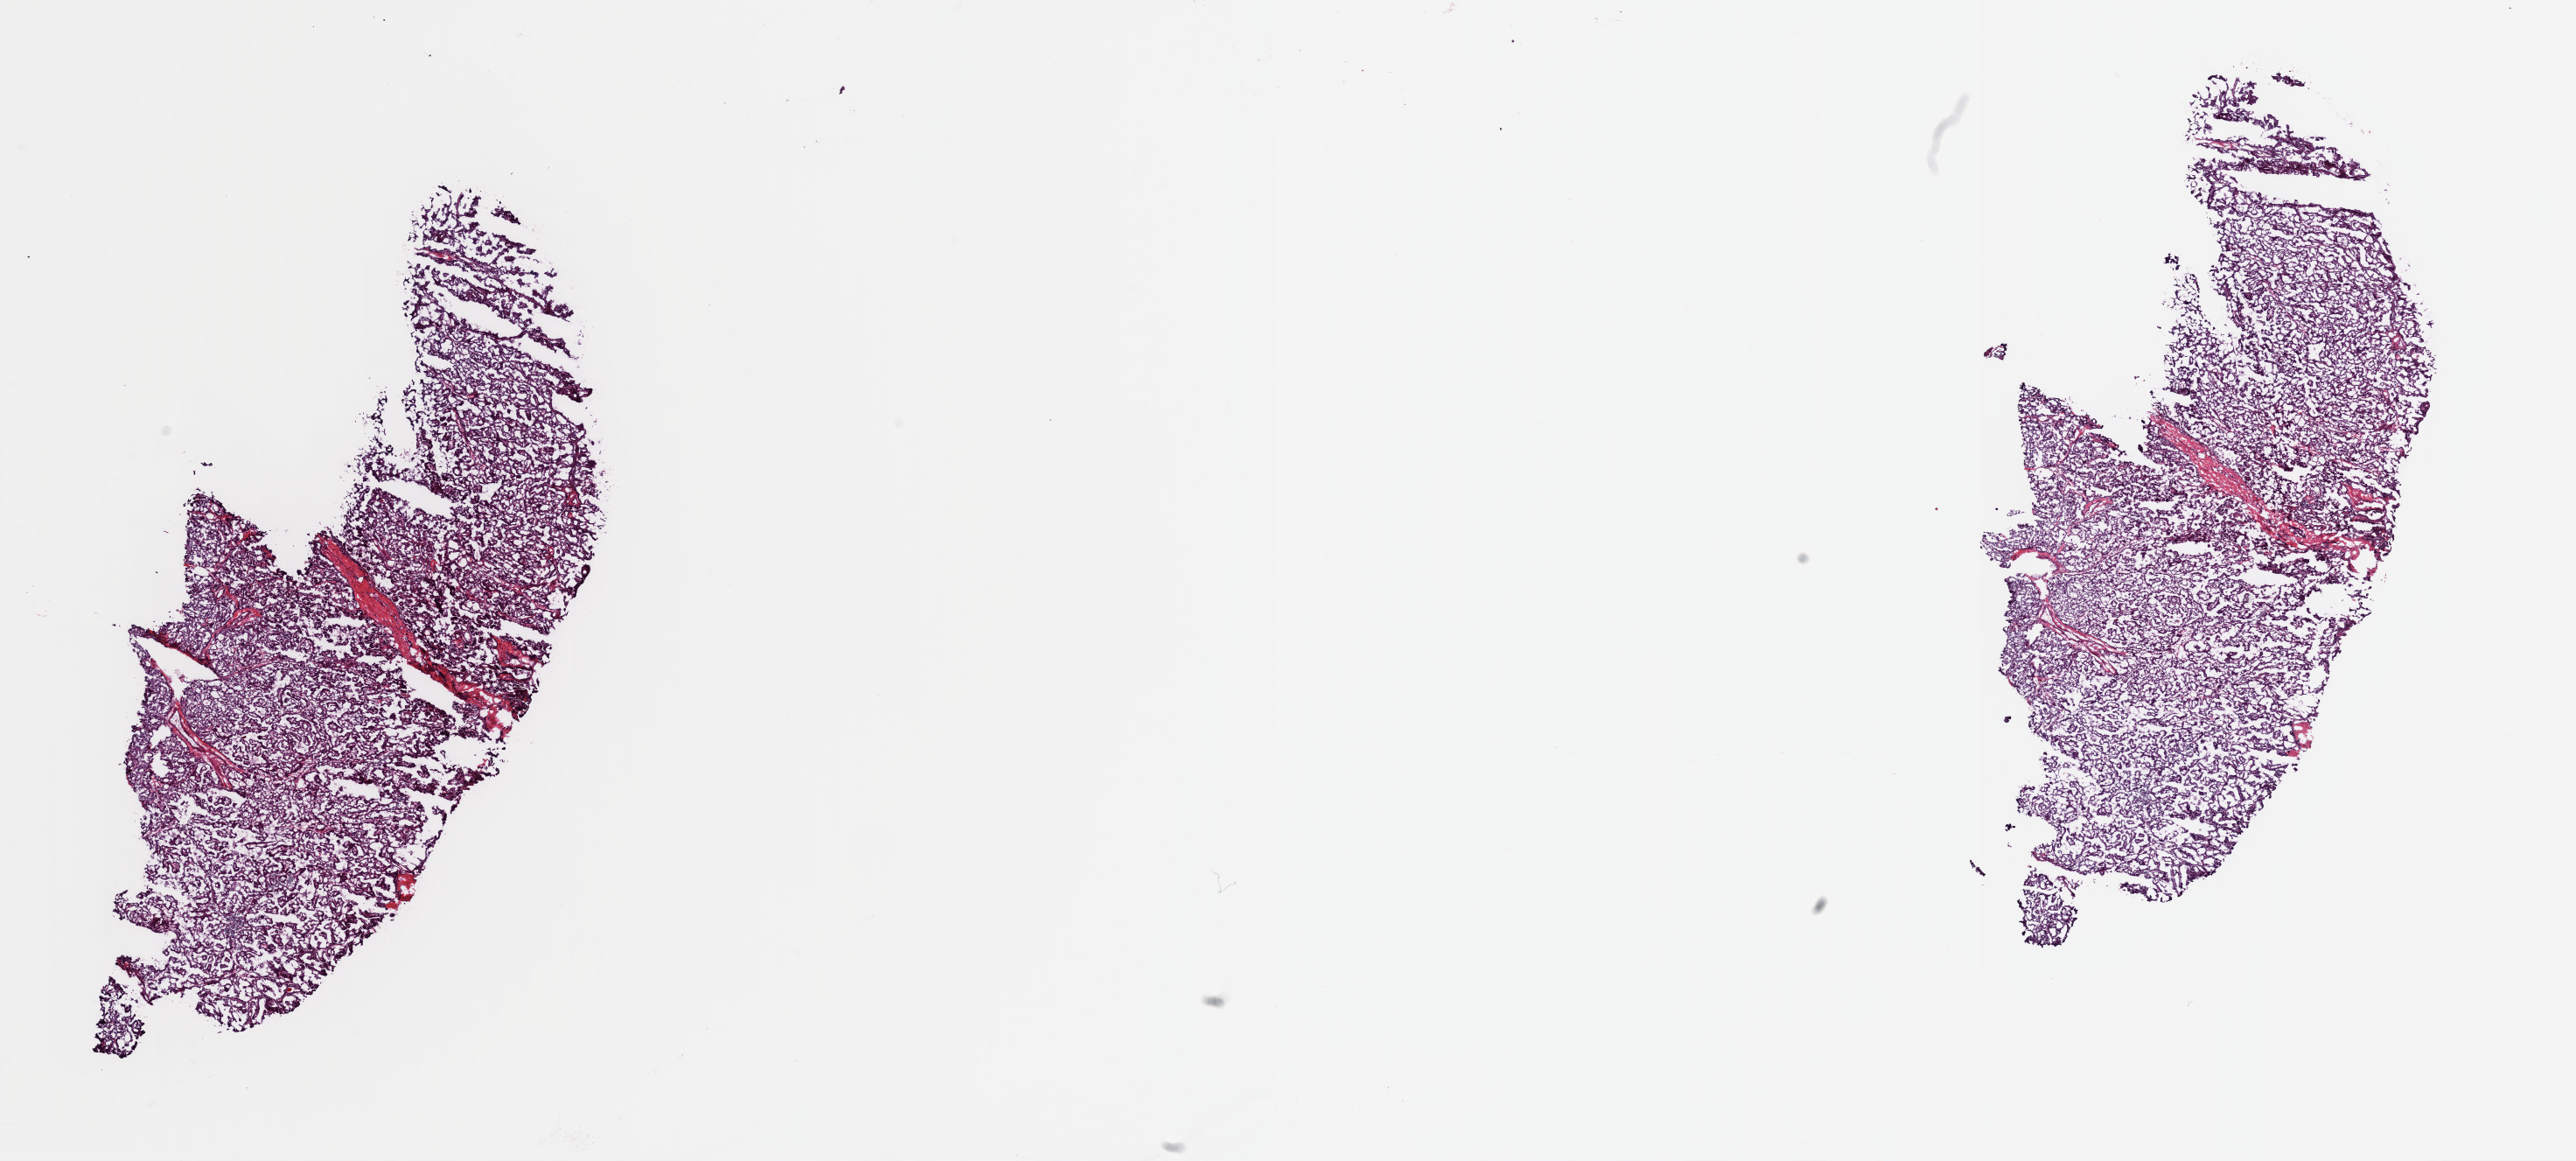
Whole-slide histology image, Hematoxylin and eosin (H&E) stained, shown as a low-resolution overview of the whole scanned area (about 23.3 x 10.5 mm); frozen section; primary tumour sample from the thyroid. Male, age 61 years at initial diagnosis. Pathologist review of this section (percent, as recorded): tumour cells 90%, tumour nuclei 95%, normal cells 0%, stromal cells 10%, necrosis 0%. Inflammatory infiltration, as recorded: lymphocyte infiltration 3%, monocyte infiltration 1%, neutrophil infiltration 0%.
TNM: T2 N1b MX. Lymph nodes positive (case pathology): 10 of 26 examined. AJCC pathologic stage: IVA. Pathologic diagnosis: Papillary adenocarcinoma, NOS (thyroid gland).